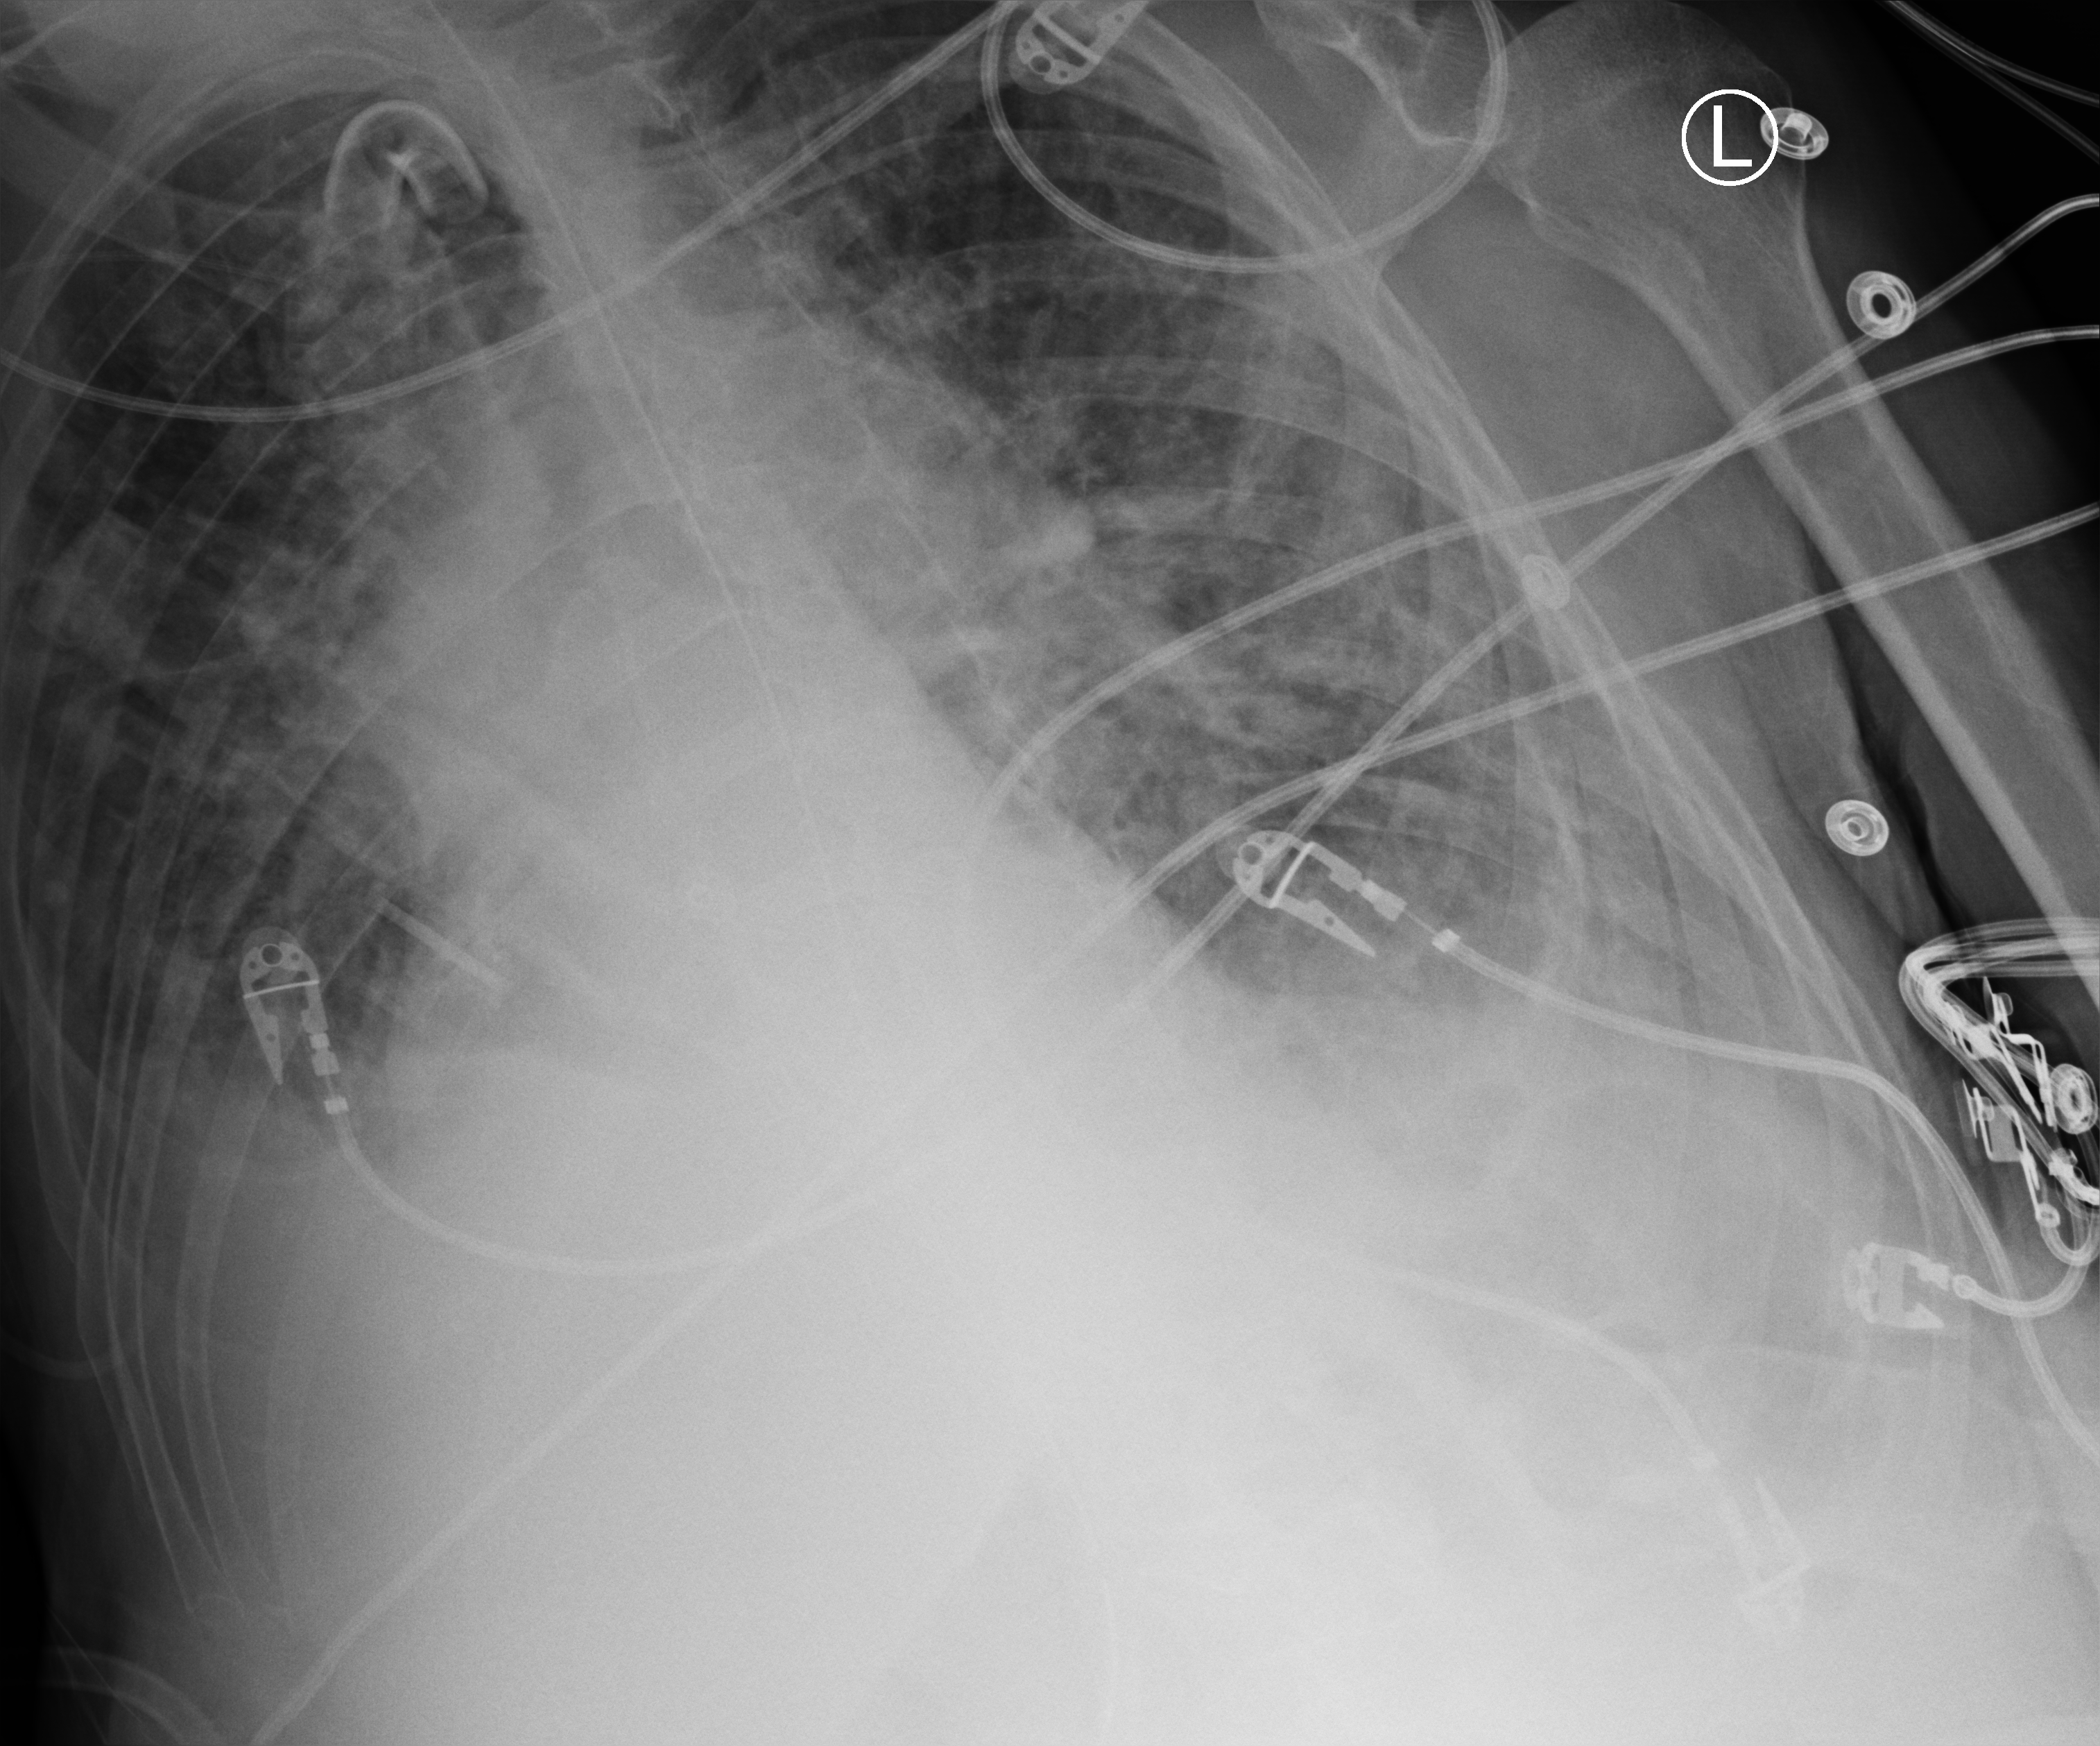
Chest X-ray (portable); anteroposterior (AP) projection. Male patient hospitalised with COVID-19, age 75–90 years.
Admission-level facts for this patient (not findings on this image; timing relative to this image not recorded): mechanically ventilated during this hospital stay: yes.